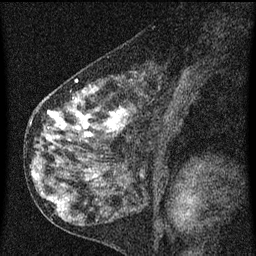
Breast MRI (dynamic contrast-enhanced), one sagittal slice; slice 33 of 60 in the series (ordered by position); dynamic contrast-enhanced series, image 2 of 3 at this slice position (ordered by acquisition); 1.5 T; TE 4.2 ms, TR 8 ms; 256 × 256 image matrix. Female patient, age 55 years.
Structures marked on this image (semi-automatic segmentation, software-assisted and operator-edited):
- analysis volume of interest (the breast-tissue region the enhancement analysis was run in; not a lesion): box from (x=42, y=72) to (x=184, y=155) px
- tumour enhancement mask (voxels above the 70 % enhancement threshold inside the analysis volume of interest): (x=48, y=80)–(x=129, y=137)